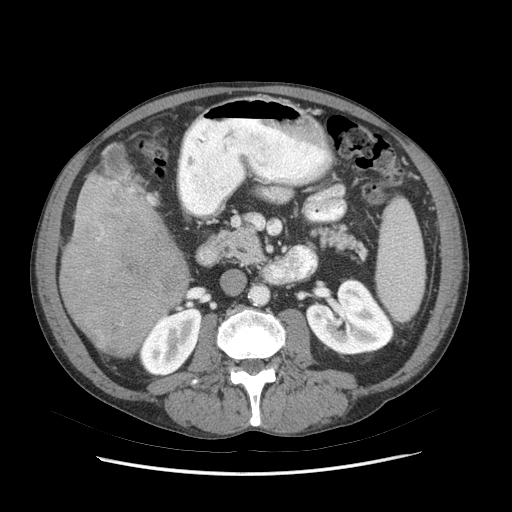
Contrast-enhanced abdominal CT (liver protocol), one axial slice. Slice 25 of 89 in the series (ordered by position). Soft-tissue window (W 400 / L 40 HU). 512 × 512 image matrix, field of view 380 × 380 mm. Case-level facts recorded for this patient, not image findings: diagnosis: hepatocellular carcinoma (patient treated with transarterial chemoembolisation; whether this scan precedes or follows treatment is not stated here); TNM stage (as recorded): Stage-IIIB; Child-Pugh class: A; tumour differentiation: moderately differentiated.
Structures marked on this image (semi-automatic segmentation, software-assisted and operator-edited):
- liver parenchyma outside the tumour (the mass and vessels are separate outlines, so this box may not span the whole liver): bounding box (x1, y1, x2, y2) in pixels: (60, 174, 188, 358)
- mass: (60, 208, 187, 357)